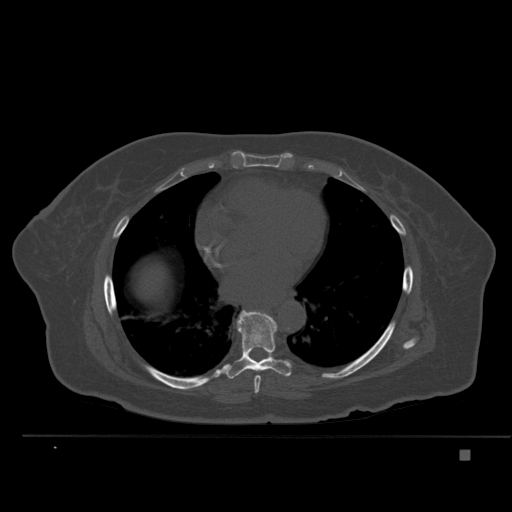
CT including the spine, one axial slice; position 313 of 477 along the scan axis; bone window (W 1800 / L 400 HU); 1.5 mm slice thickness; 512 × 512 image matrix, field of view 422 × 422 mm. Female patient, age 74 years. Case-level facts recorded for this patient, not image findings: primary cancer: colon.
Outlined on this slice (semi-automatically segmented with operator editing):
- T7 vertebra: box from (x=254, y=376) to (x=261, y=393) px
- T8 vertebra: (x=219, y=310)–(x=291, y=379)